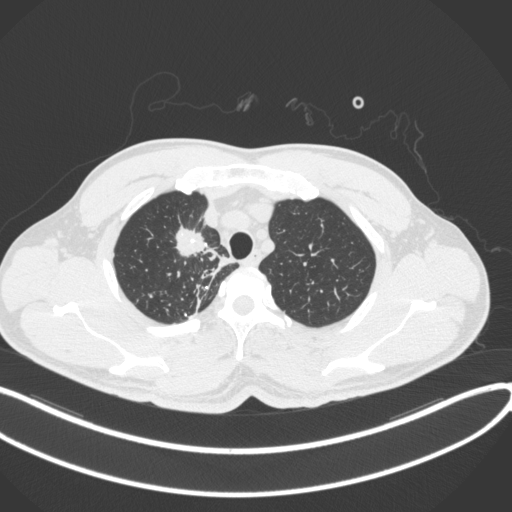
Chest CT, one axial slice; slice 315 of 391 in the series (ordered by position); reconstruction kernel B31f; lung window (W 1500 / L -600 HU); 1 mm slice thickness; 512 × 512 image matrix, field of view 400 × 400 mm. Patient: male, 48 years. Case-level facts recorded for this patient, not image findings: clinical TNM (as recorded): T1c N1 M1.
Outlined on this slice (bounding box drawn by a radiologist):
- lung tumour (recorded histology: adenocarcinoma): bounding box <170,221,209,261> (left, top, right, bottom; pixels)